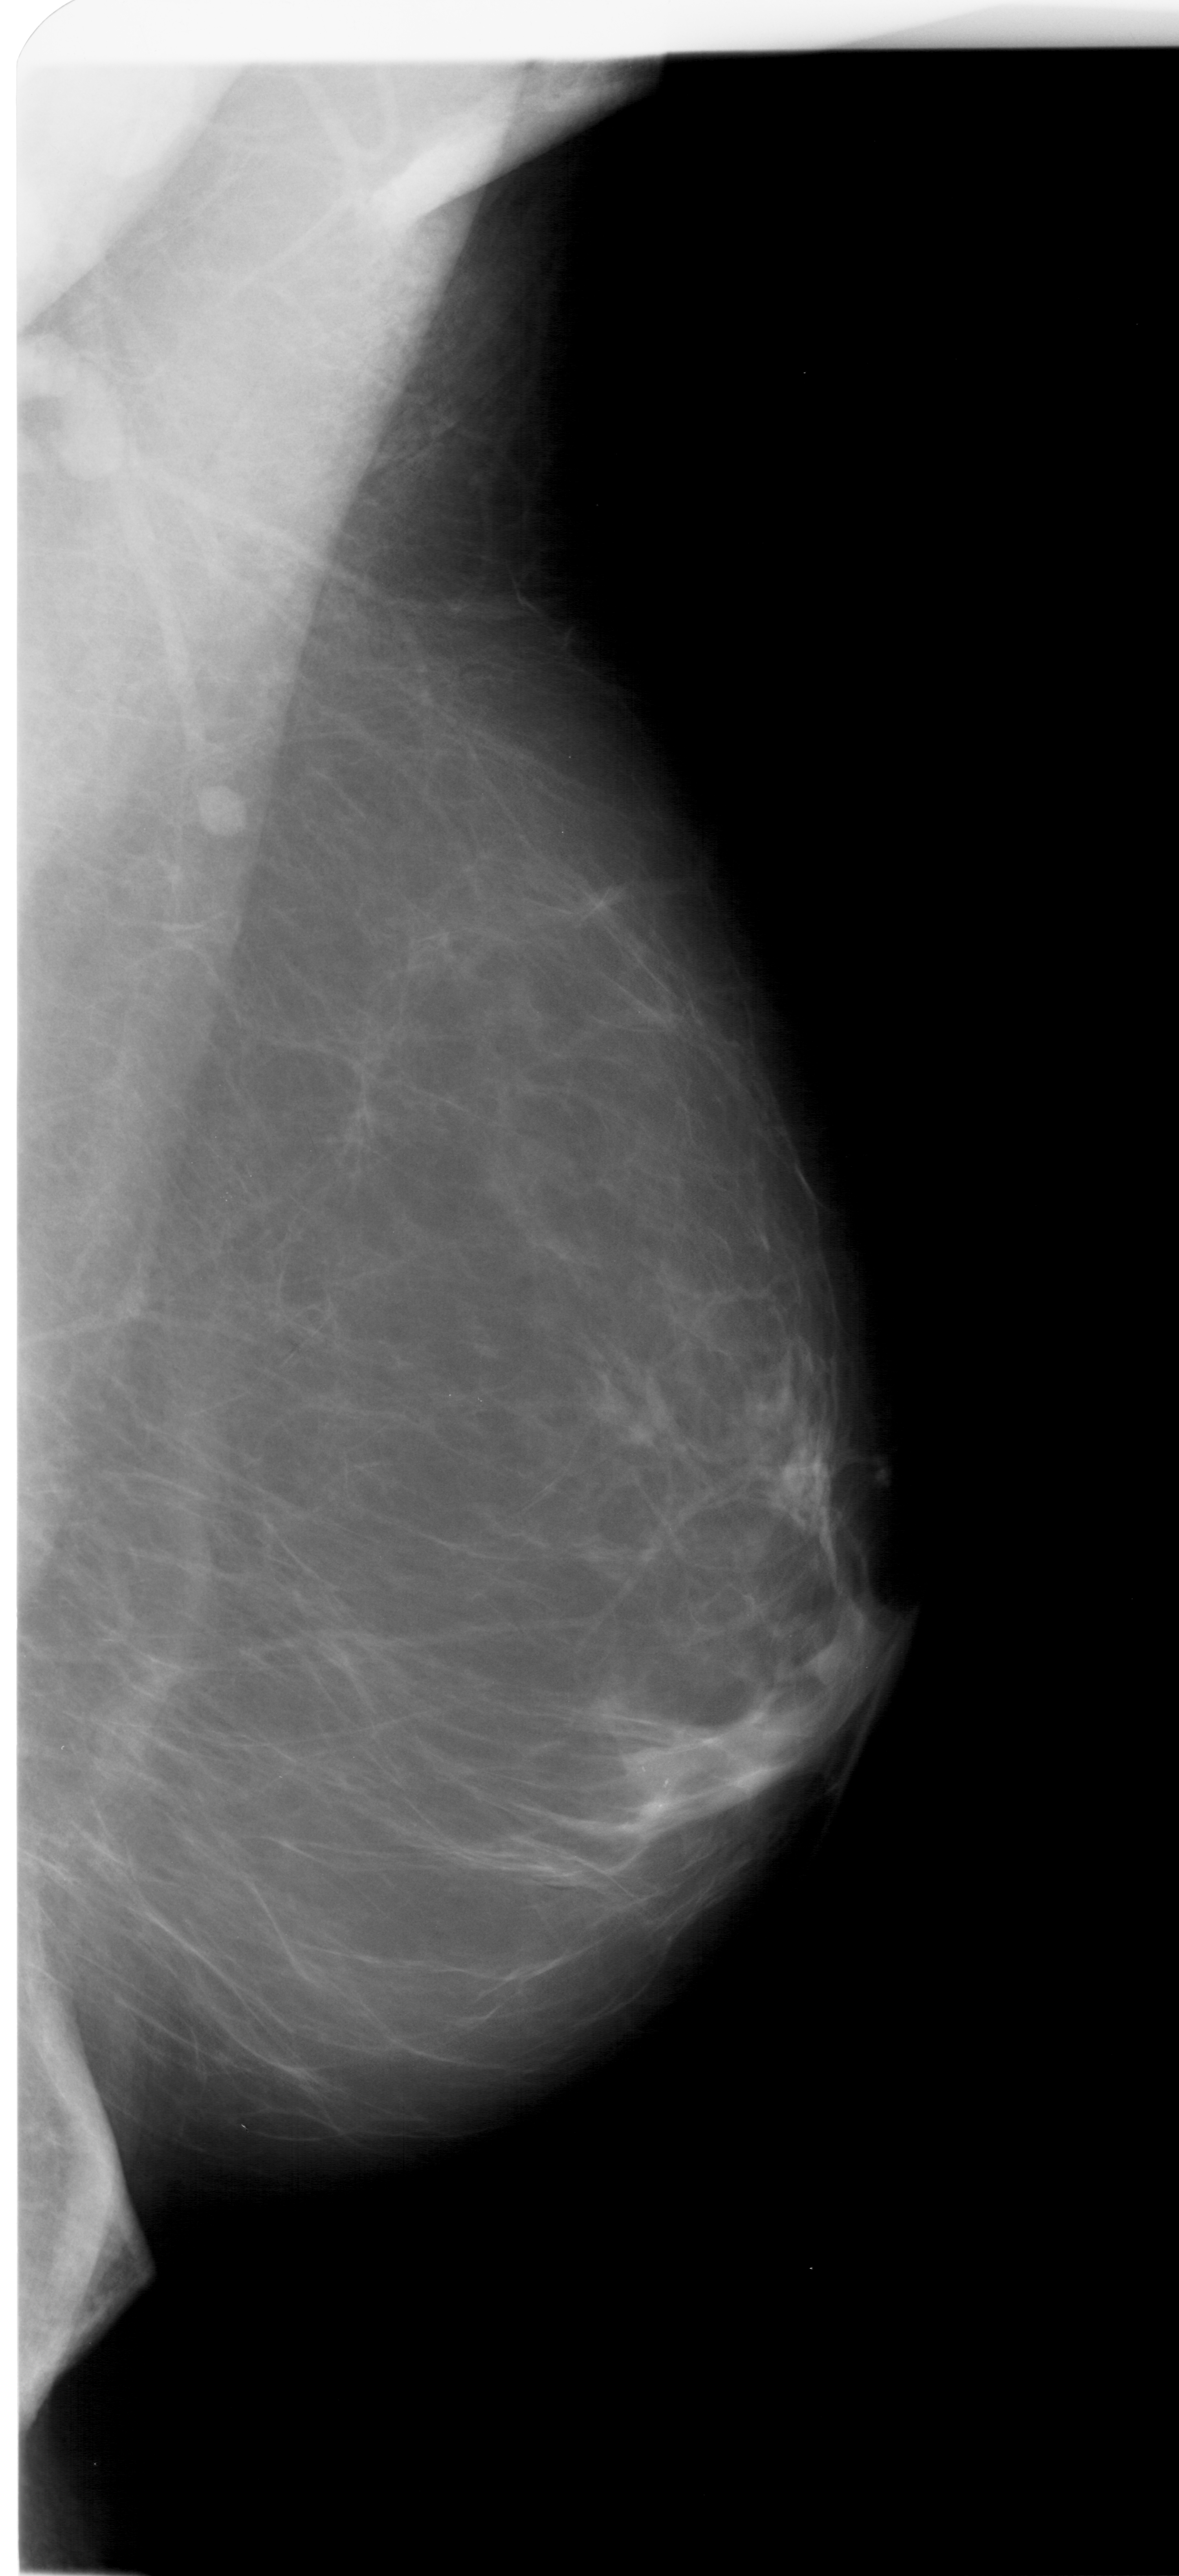
Mammogram (digitized film), right breast, MLO view.
Calcifications, morphology pleomorphic, distribution clustered; BI-RADS assessment category 4; subtlety rating 3 on a 1 (subtle) to 5 (obvious) scale; pathology result (as recorded, not read from the image): malignant.